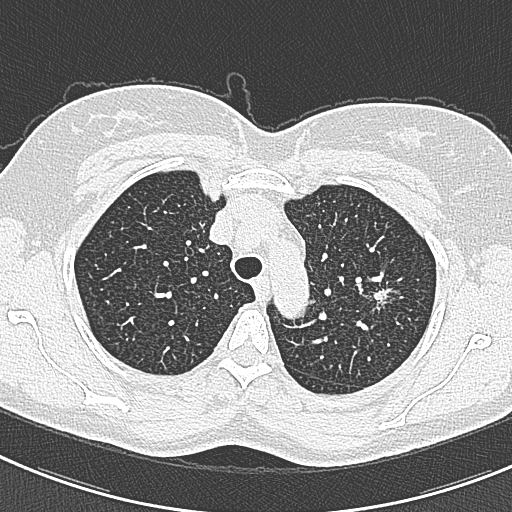
Low-dose screening chest CT, axial slice; baseline screening round; lung window (W 1500 / L -600 HU); 1 mm slice thickness; lung (sharp) reconstruction kernel (B80f); 120 kVp; 512 × 512 image matrix. Female participant, aged 57 years at enrolment. Current smoker at enrolment.
Lesion marked by an expert reader, bounding box (x1, y1, x2, y2) in pixels: (362, 273, 412, 322). The screening reader recorded 2 non-calcified nodules or masses ≥4 mm on this exam (right lower lobe, left upper lobe); which of them this box marks is not recorded. Participant outcome: lung cancer diagnosed 198 days after this screen — adenocarcinoma, NOS, left upper lobe, well differentiated (G1), stage IA (AJCC 6th edition), 10 mm at pathology.